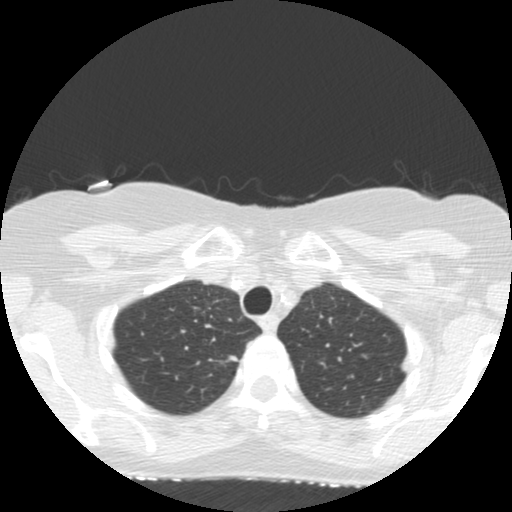
Low-dose screening chest CT, one axial slice. Position 128 of 155 along the scan axis. Reconstruction kernel STANDARD. 120 kVp. Lung window (W 1500 / L -600 HU). 512 × 512 image matrix, field of view 300 × 300 mm.
Annotated regions visible in this slice (outlined manually by an expert reader):
- lesion 1 (tumor, upper lobe of right lung): bounding box <226,355,238,362> (left, top, right, bottom; pixels)